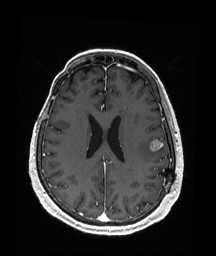
Brain MRI from a brain-tumour surgery series, one axial slice; position 75 of 176 along the scan axis; T1-weighted post-contrast; 216 × 256 image matrix, field of view 211 × 250 mm. From the clinical record (not read from this slice): histopathology: Metastatic Malignant Melanoma; tumour location: Left Frontal.
Structures marked on this image (outlined manually by an expert reader):
- tumour: box from (x=149, y=139) to (x=163, y=152) px